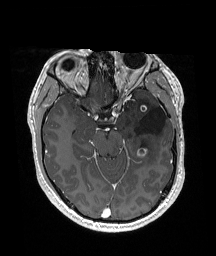
Brain MRI from a brain-tumour surgery series, one axial slice. Slice 110 of 192 in the series (ordered by position). T1-weighted post-contrast. 1 mm slice thickness. 216 × 256 image matrix. From the clinical record (not read from this slice): histopathology: Glioneuronal tumor; WHO grade: 2; tumour location: Left Superior Temporal Gyrus.
Structures marked on this image (manually delineated by an expert):
- previous resection cavity: box from (x=135, y=106) to (x=166, y=134) px
- tumour: (x=137, y=104)–(x=148, y=158)